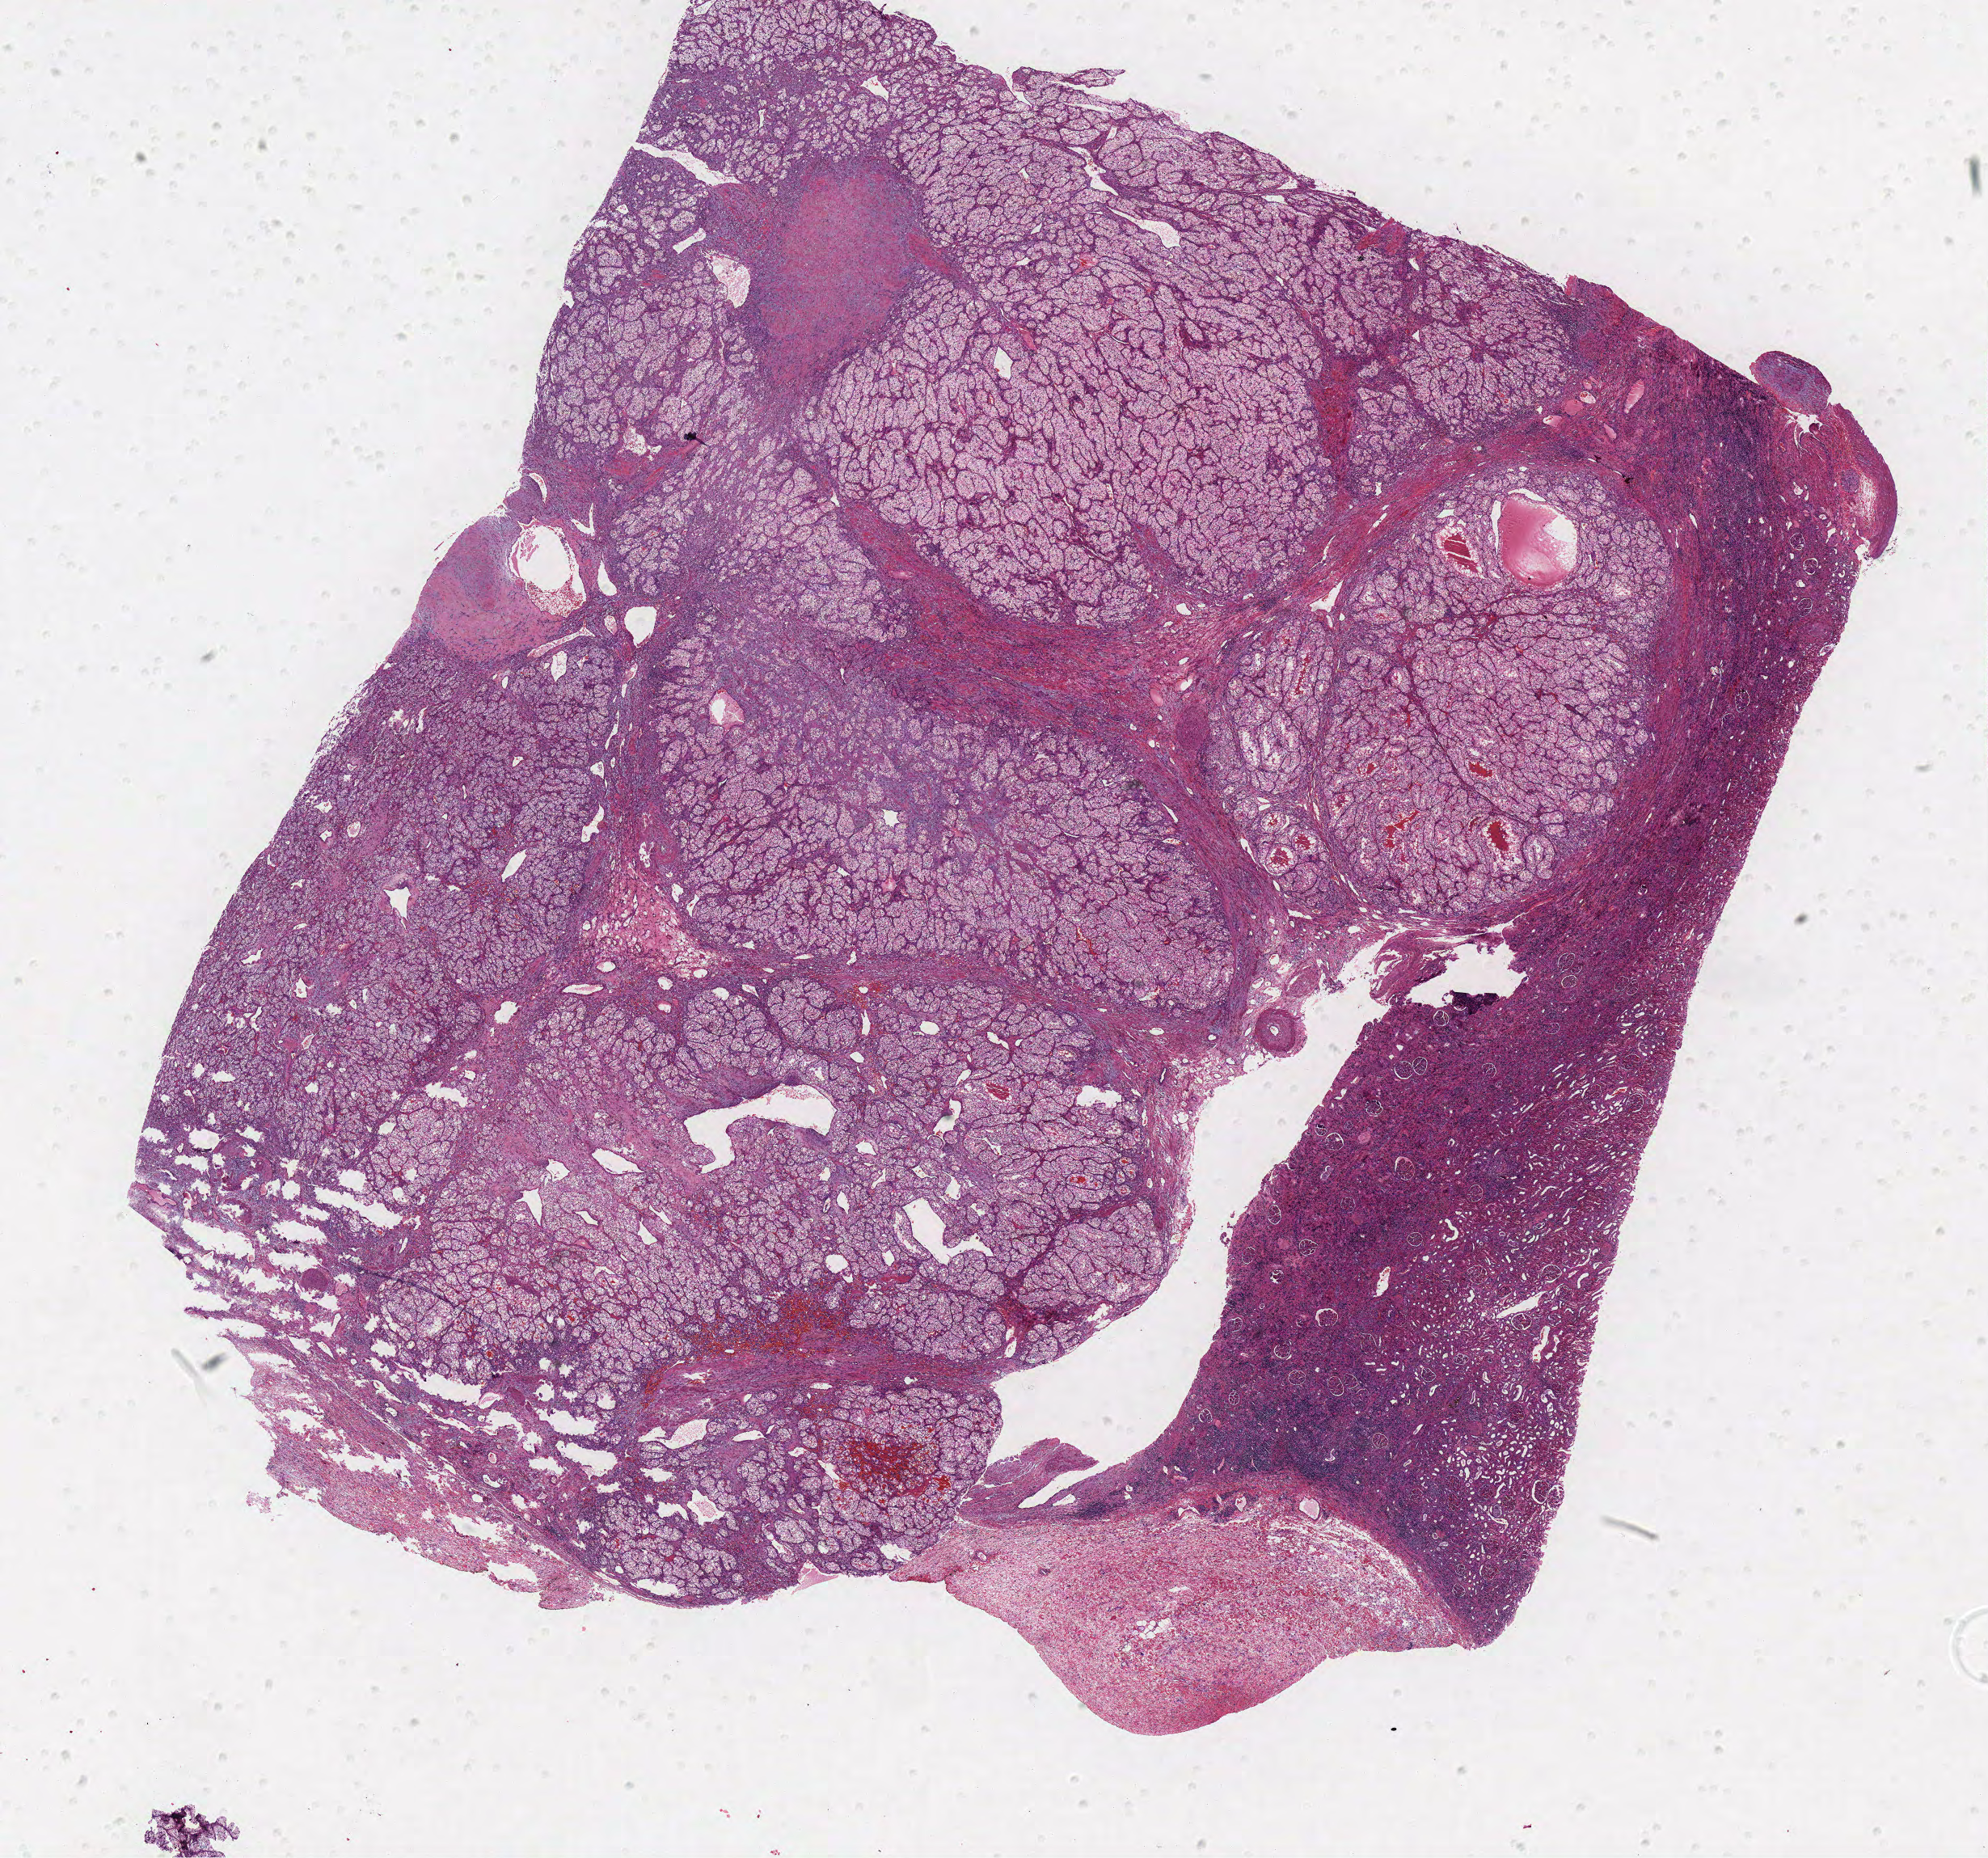
Digitized Hematoxylin and eosin (H&E) stained tissue section (whole slide) — a low-resolution overview of the entire scanned area, about 19.7 x 18.4 mm (acquisition: 40x scan), FFPE section, kidney, primary tumour sample. Patient: male, age at initial diagnosis 62 years. Histologic grade: G3 (poorly differentiated).
AJCC pathologic stage: III. Diagnosis: Clear cell adenocarcinoma, NOS. Lymph nodes positive (case pathology): 0 of 1 examined. TNM: T3b N0 M0.